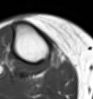
MRI of an extremity soft-tissue mass, one axial slice. Position 38 of 54 along the scan axis. MR volume resampled by the dataset authors to the PET/CT grid (not the native acquisition matrix). 3.27 mm slice thickness. 93 × 99 image matrix. Female patient. Case-level facts recorded for this patient, not image findings: histological type: undifferentiated – high grade; grade: high; site of the primary tumour: right thigh.
Annotated regions visible in this slice (expert contour drawn on MRI and transferred to this co-registered scan by the dataset authors):
- gross tumour volume (mass): box from (x=48, y=48) to (x=62, y=69) px